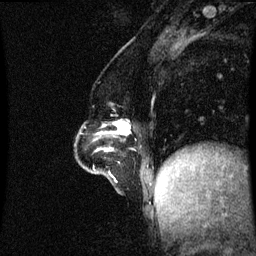
Breast MRI (dynamic contrast-enhanced), one sagittal slice. Position 22 of 60 along the scan axis. Dynamic contrast-enhanced series, image 2 of 3 at this slice position (ordered by acquisition). 1.5 T. TE 4.2 ms, TR 8.9 ms. 2.1 mm slice thickness. 256 × 256 image matrix. Patient: female, 47 years. From the clinical record (not read from this slice): setting: breast cancer imaged before/during neoadjuvant chemotherapy; receptor status: HR-positive, HER2-negative.
Outlined on this slice (semi-automatically segmented with operator editing):
- analysis volume of interest (the breast-tissue region the enhancement analysis was run in; not a lesion): bounding box (x1, y1, x2, y2) in pixels: (76, 114, 131, 163)
- tumour enhancement mask (voxels above the 70 % enhancement threshold inside the analysis volume of interest): (114, 122, 131, 135)